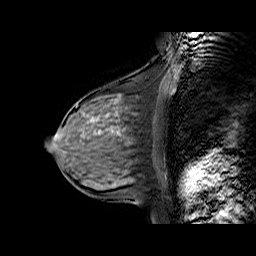
Breast MRI (dynamic contrast-enhanced), one sagittal slice. Slice 29 of 60 in the series (ordered by position). Dynamic contrast-enhanced series, time point 2 of 6 at this slice position (early post-contrast). 1.5 T. TE 6.3 ms, TR 32.9 ms. 256 × 256 image matrix, field of view 200 × 200 mm. Female patient. From the clinical record (not read from this slice): setting: breast cancer imaged before/during neoadjuvant chemotherapy; receptor status: HR-positive, HER2-negative.
Structures marked on this image (semi-automatically segmented with operator editing):
- analysis volume of interest (the breast-tissue region the enhancement analysis was run in; not a lesion): bounding box [x1, y1, x2, y2] px = [57, 86, 168, 170]
- tumour enhancement mask (voxels above the 100 % enhancement threshold inside the analysis volume of interest): [108, 114, 120, 135]